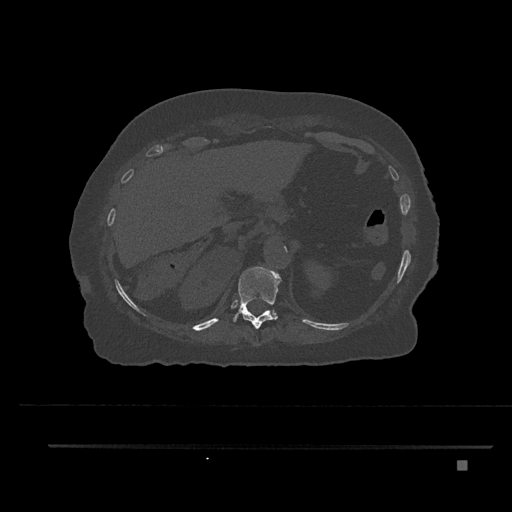
CT including the spine, one axial slice. Slice 309 of 797 in the series (ordered by position). Reconstruction kernel Br40s/3. 120 kVp. Bone window (W 1800 / L 400 HU). 0.5 mm slice thickness. 512 × 512 image matrix, field of view 437 × 437 mm. Patient: female, 76 years. Case-level facts recorded for this patient, not image findings: primary cancer: lung.
Structures marked on this image (semi-automatic segmentation, software-assisted and operator-edited):
- T11 vertebra: bounding box (x1, y1, x2, y2) in pixels: (233, 267, 281, 329)